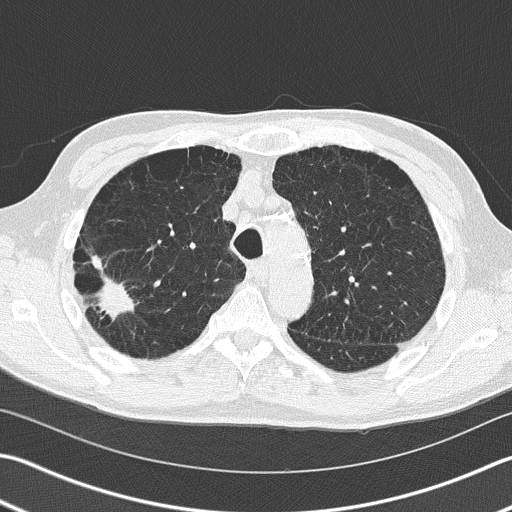
Chest CT (low-dose screening protocol), one axial image. First (baseline) screen. Lung window (W 1500 / L -600 HU). 2 mm slice thickness. 512 × 512 image matrix. Male participant, aged 66 years at enrolment. Current smoker at enrolment.
Expert reader's lesion annotation, bounding box <72,254,140,339> (left, top, right, bottom; pixels). Reader record for this screening exam (exam-level; its link to the box is not recorded): non-calcified nodule or mass ≥4 mm, right upper lobe, 39 × 23 mm, spiculated (stellate) margins, soft tissue attenuation. Lung cancer was diagnosed 36 days after this screen: squamous cell carcinoma, NOS, right upper lobe, poorly differentiated (G3), stage IB (AJCC 6th edition), 23 mm at pathology.